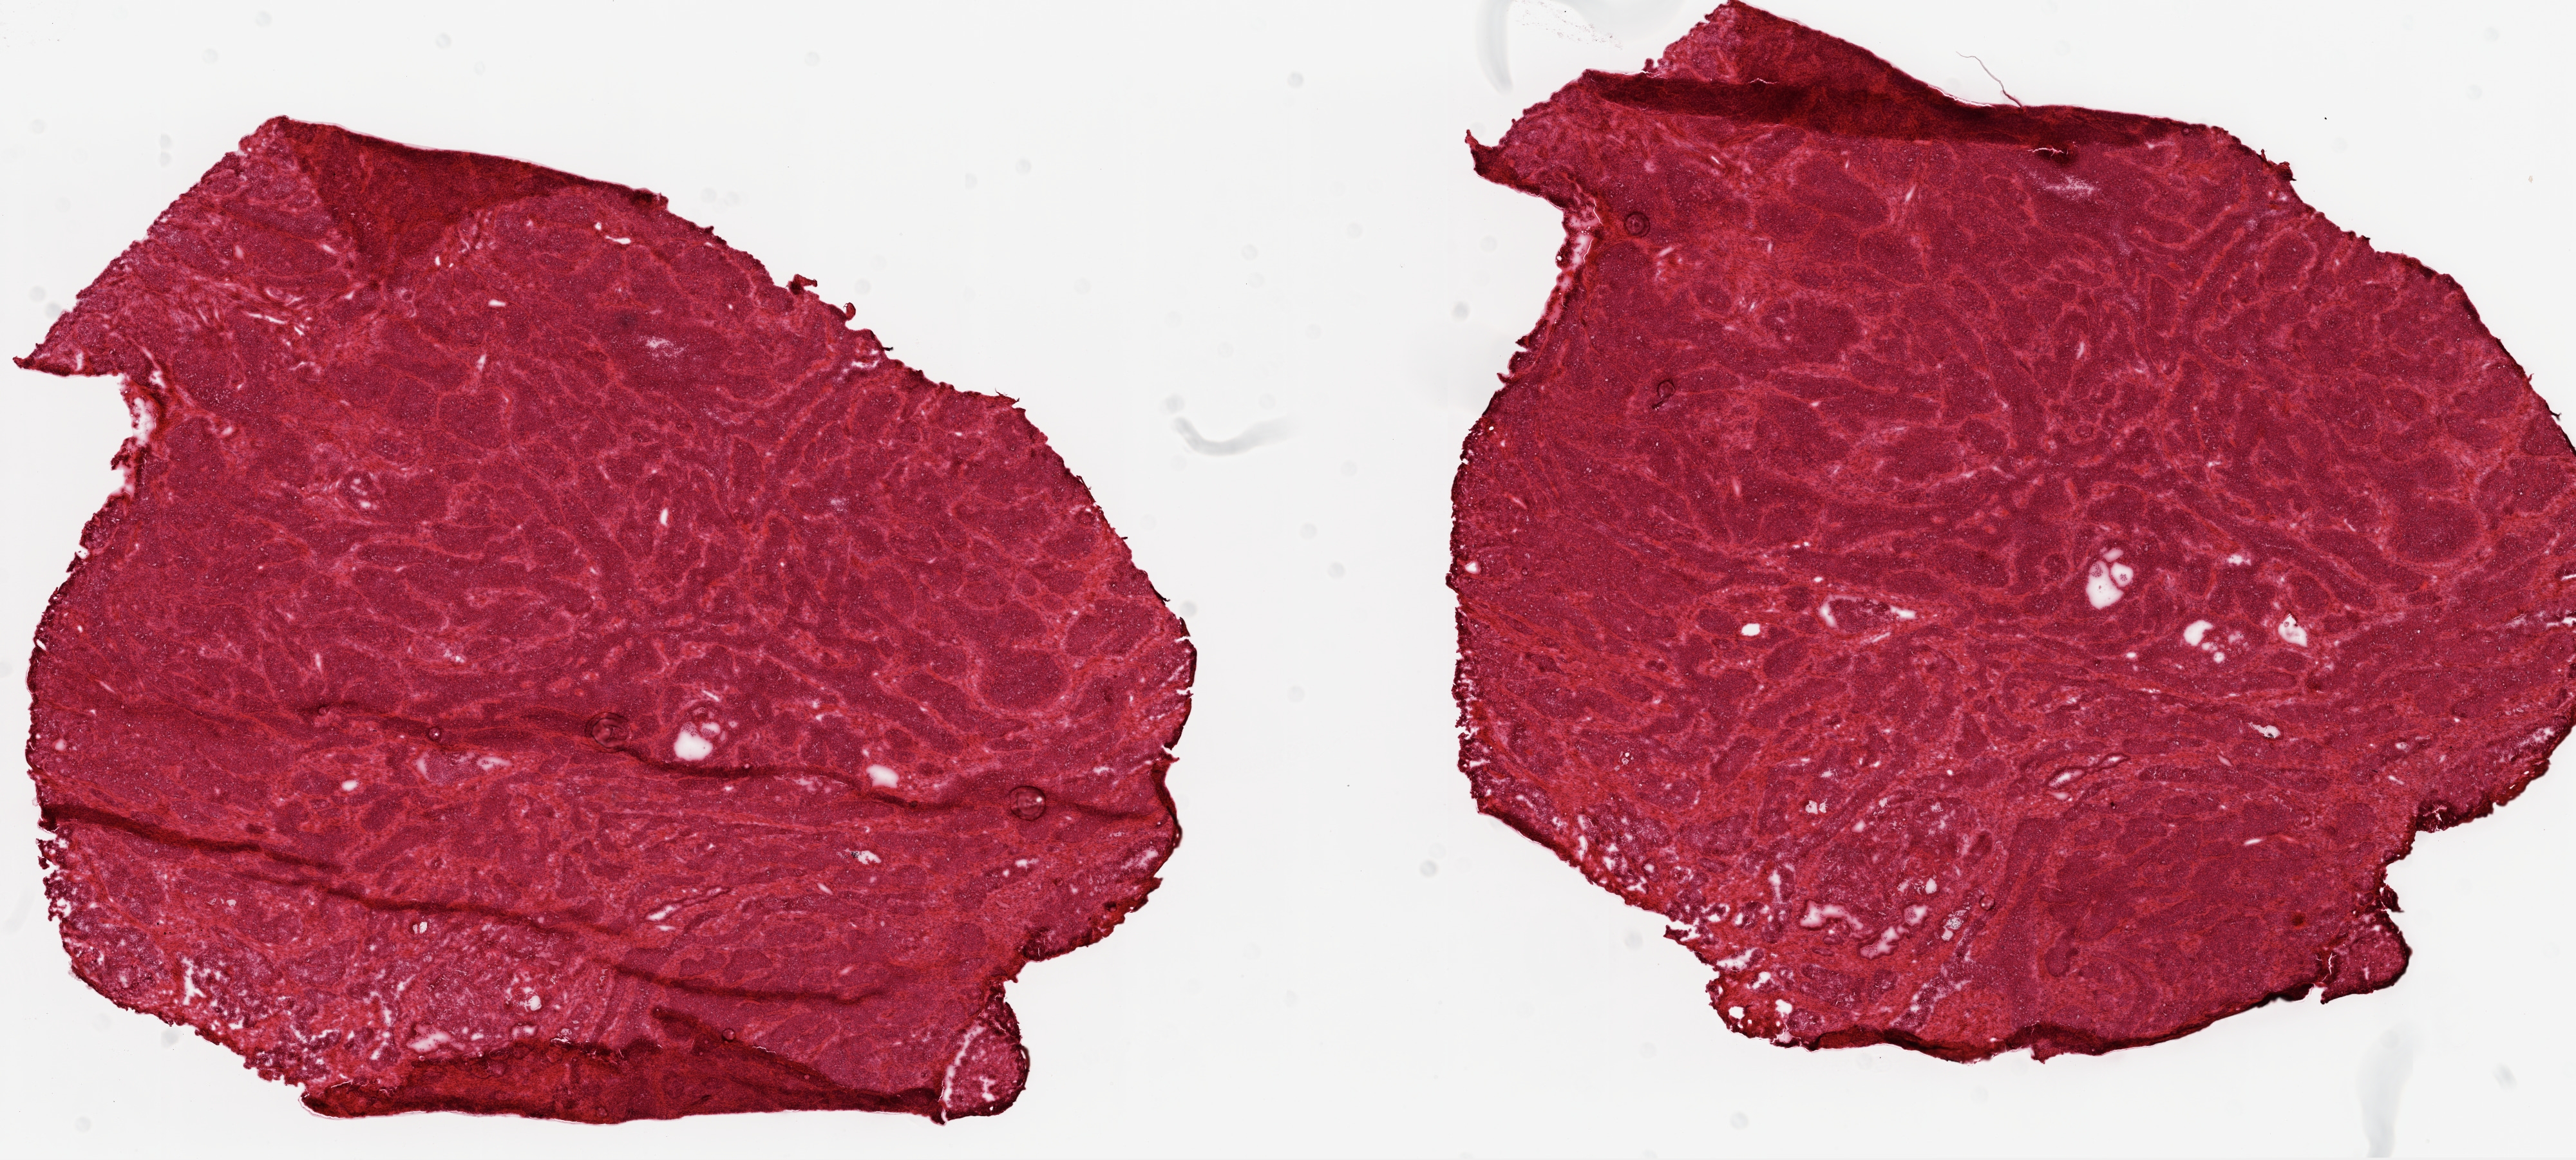
Whole-slide histology image, Hematoxylin and eosin (H&E) stained, whole scanned area (about 16.0 x 7.2 mm, slide scanned at 20x) shown as a low-resolution overview; frozen section from the top of the tissue portion; sample: primary tumour, ovary. Female, age 74 years at initial diagnosis.
Pathologic diagnosis: Serous cystadenocarcinoma, NOS.